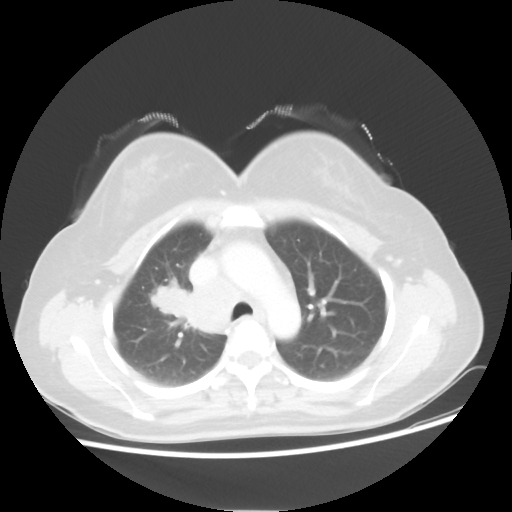
Chest CT, one axial slice. Slice 36 of 50 in the series (ordered by position). Reconstruction kernel STANDARD. 100 kVp. Lung window (W 1500 / L -600 HU). 5 mm slice thickness. 512 × 512 image matrix. Patient: female, 40 years. From the clinical record (not read from this slice): clinical TNM (as recorded): T1c N3 M0; histopathological grade: G3.
Outlined on this slice (rectangle marked by the reading radiologist):
- lung tumour (recorded histology: small cell carcinoma): bounding box <147,280,191,324> (left, top, right, bottom; pixels)